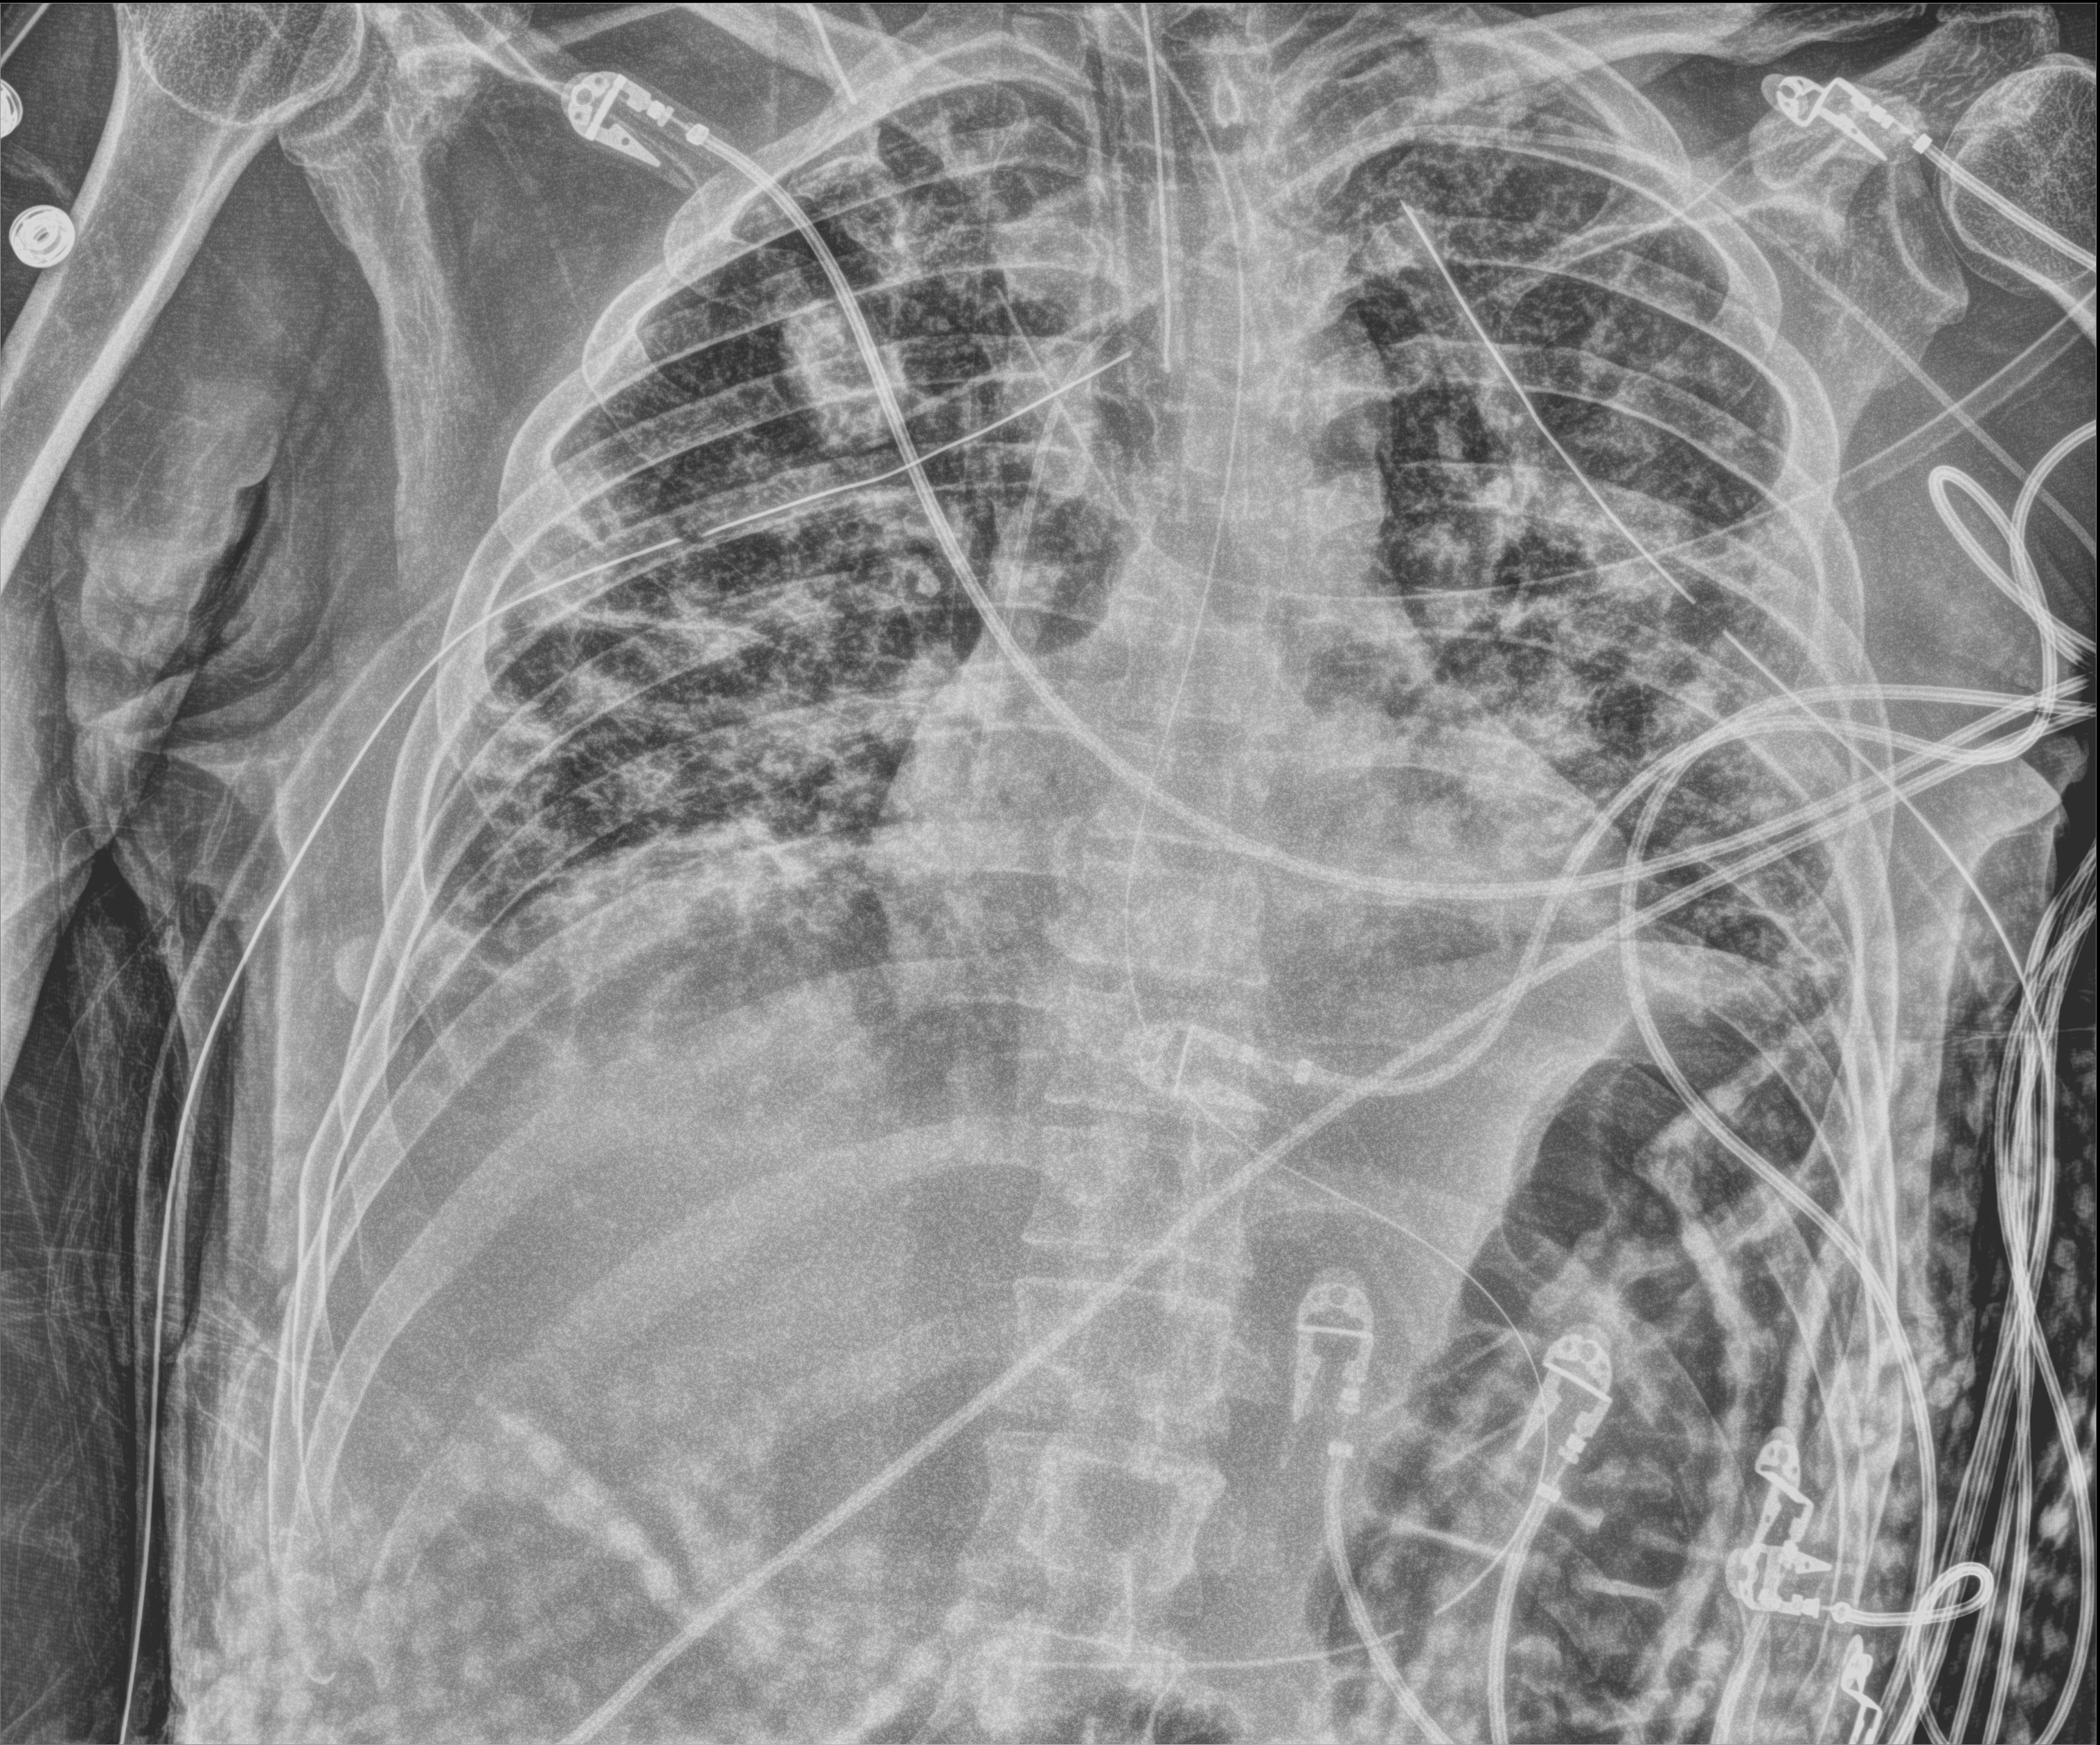
Portable chest radiograph; anteroposterior (AP) projection. Patient hospitalised with COVID-19; male, aged 18–59 years.
Admission-level facts for this patient (not findings on this image; timing relative to this image not recorded): length of hospital stay: 96 days.